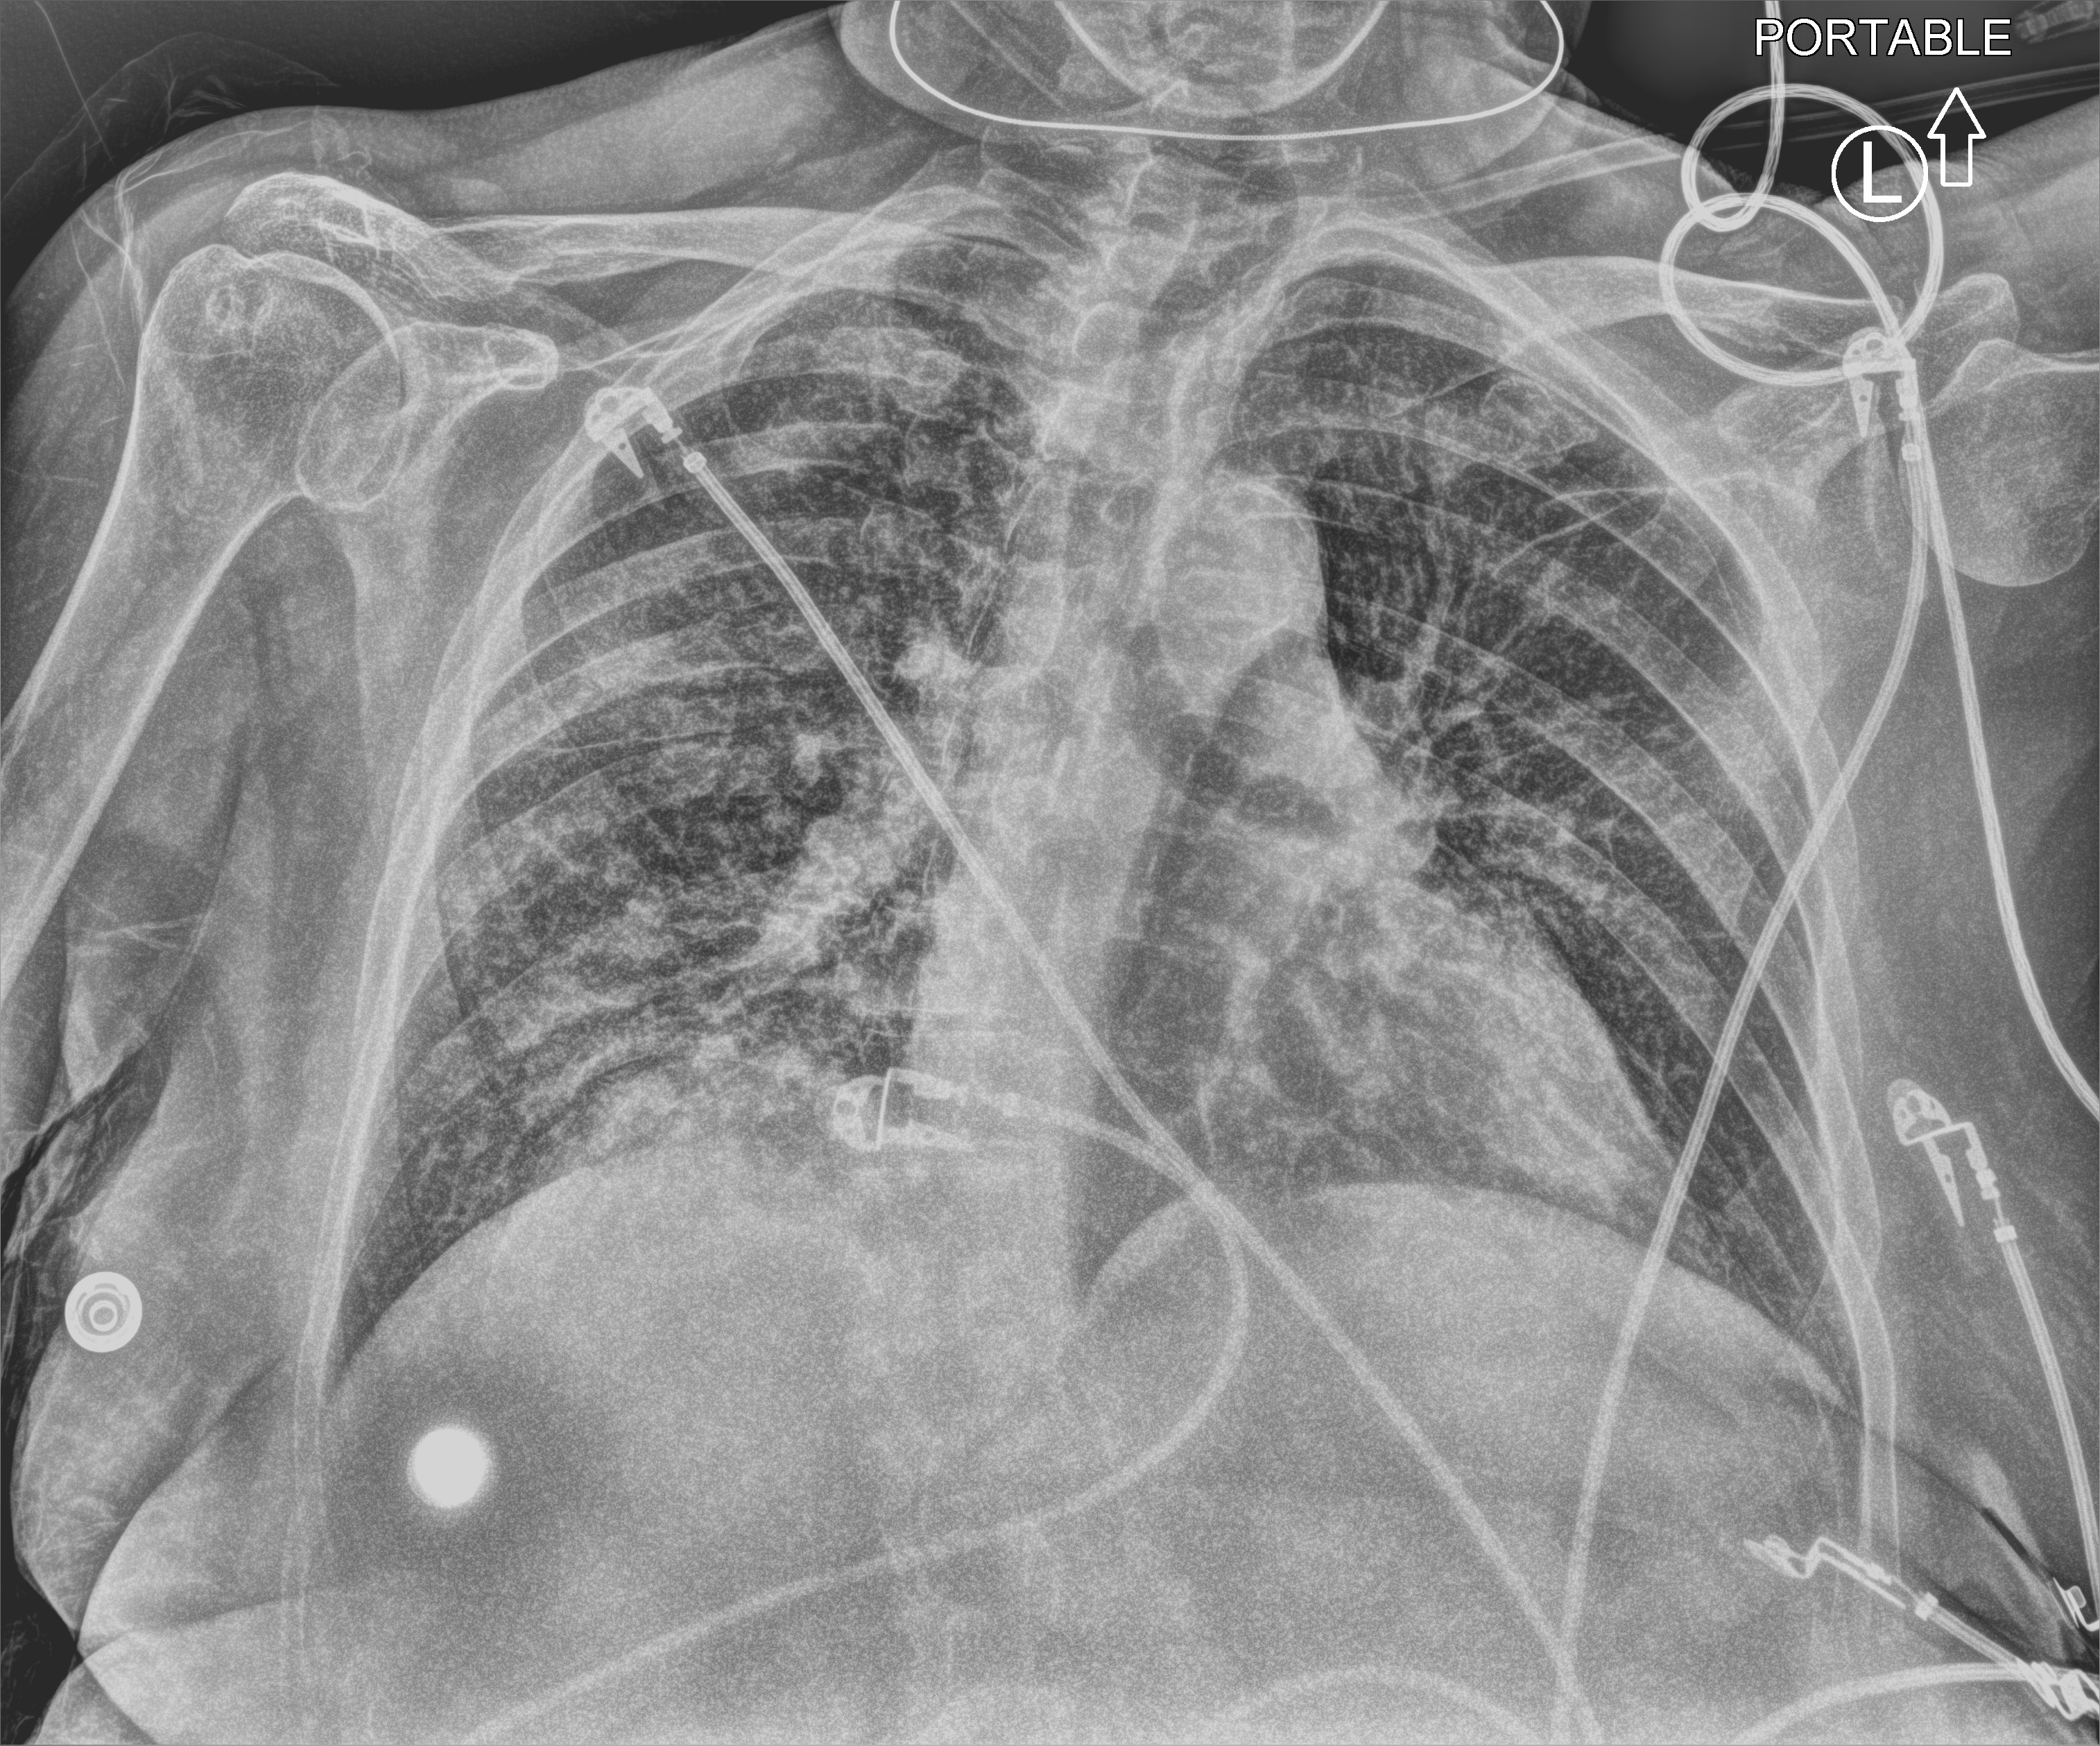
Chest X-ray (portable); anteroposterior (AP) projection. Patient hospitalised with COVID-19; female, aged 75–90 years.
Hospital-stay facts (about this admission, not read from this image; timing relative to this image not recorded):
- length of hospital stay: 28 days
- mechanically ventilated during this hospital stay: yes
- smoking status (admission record): former